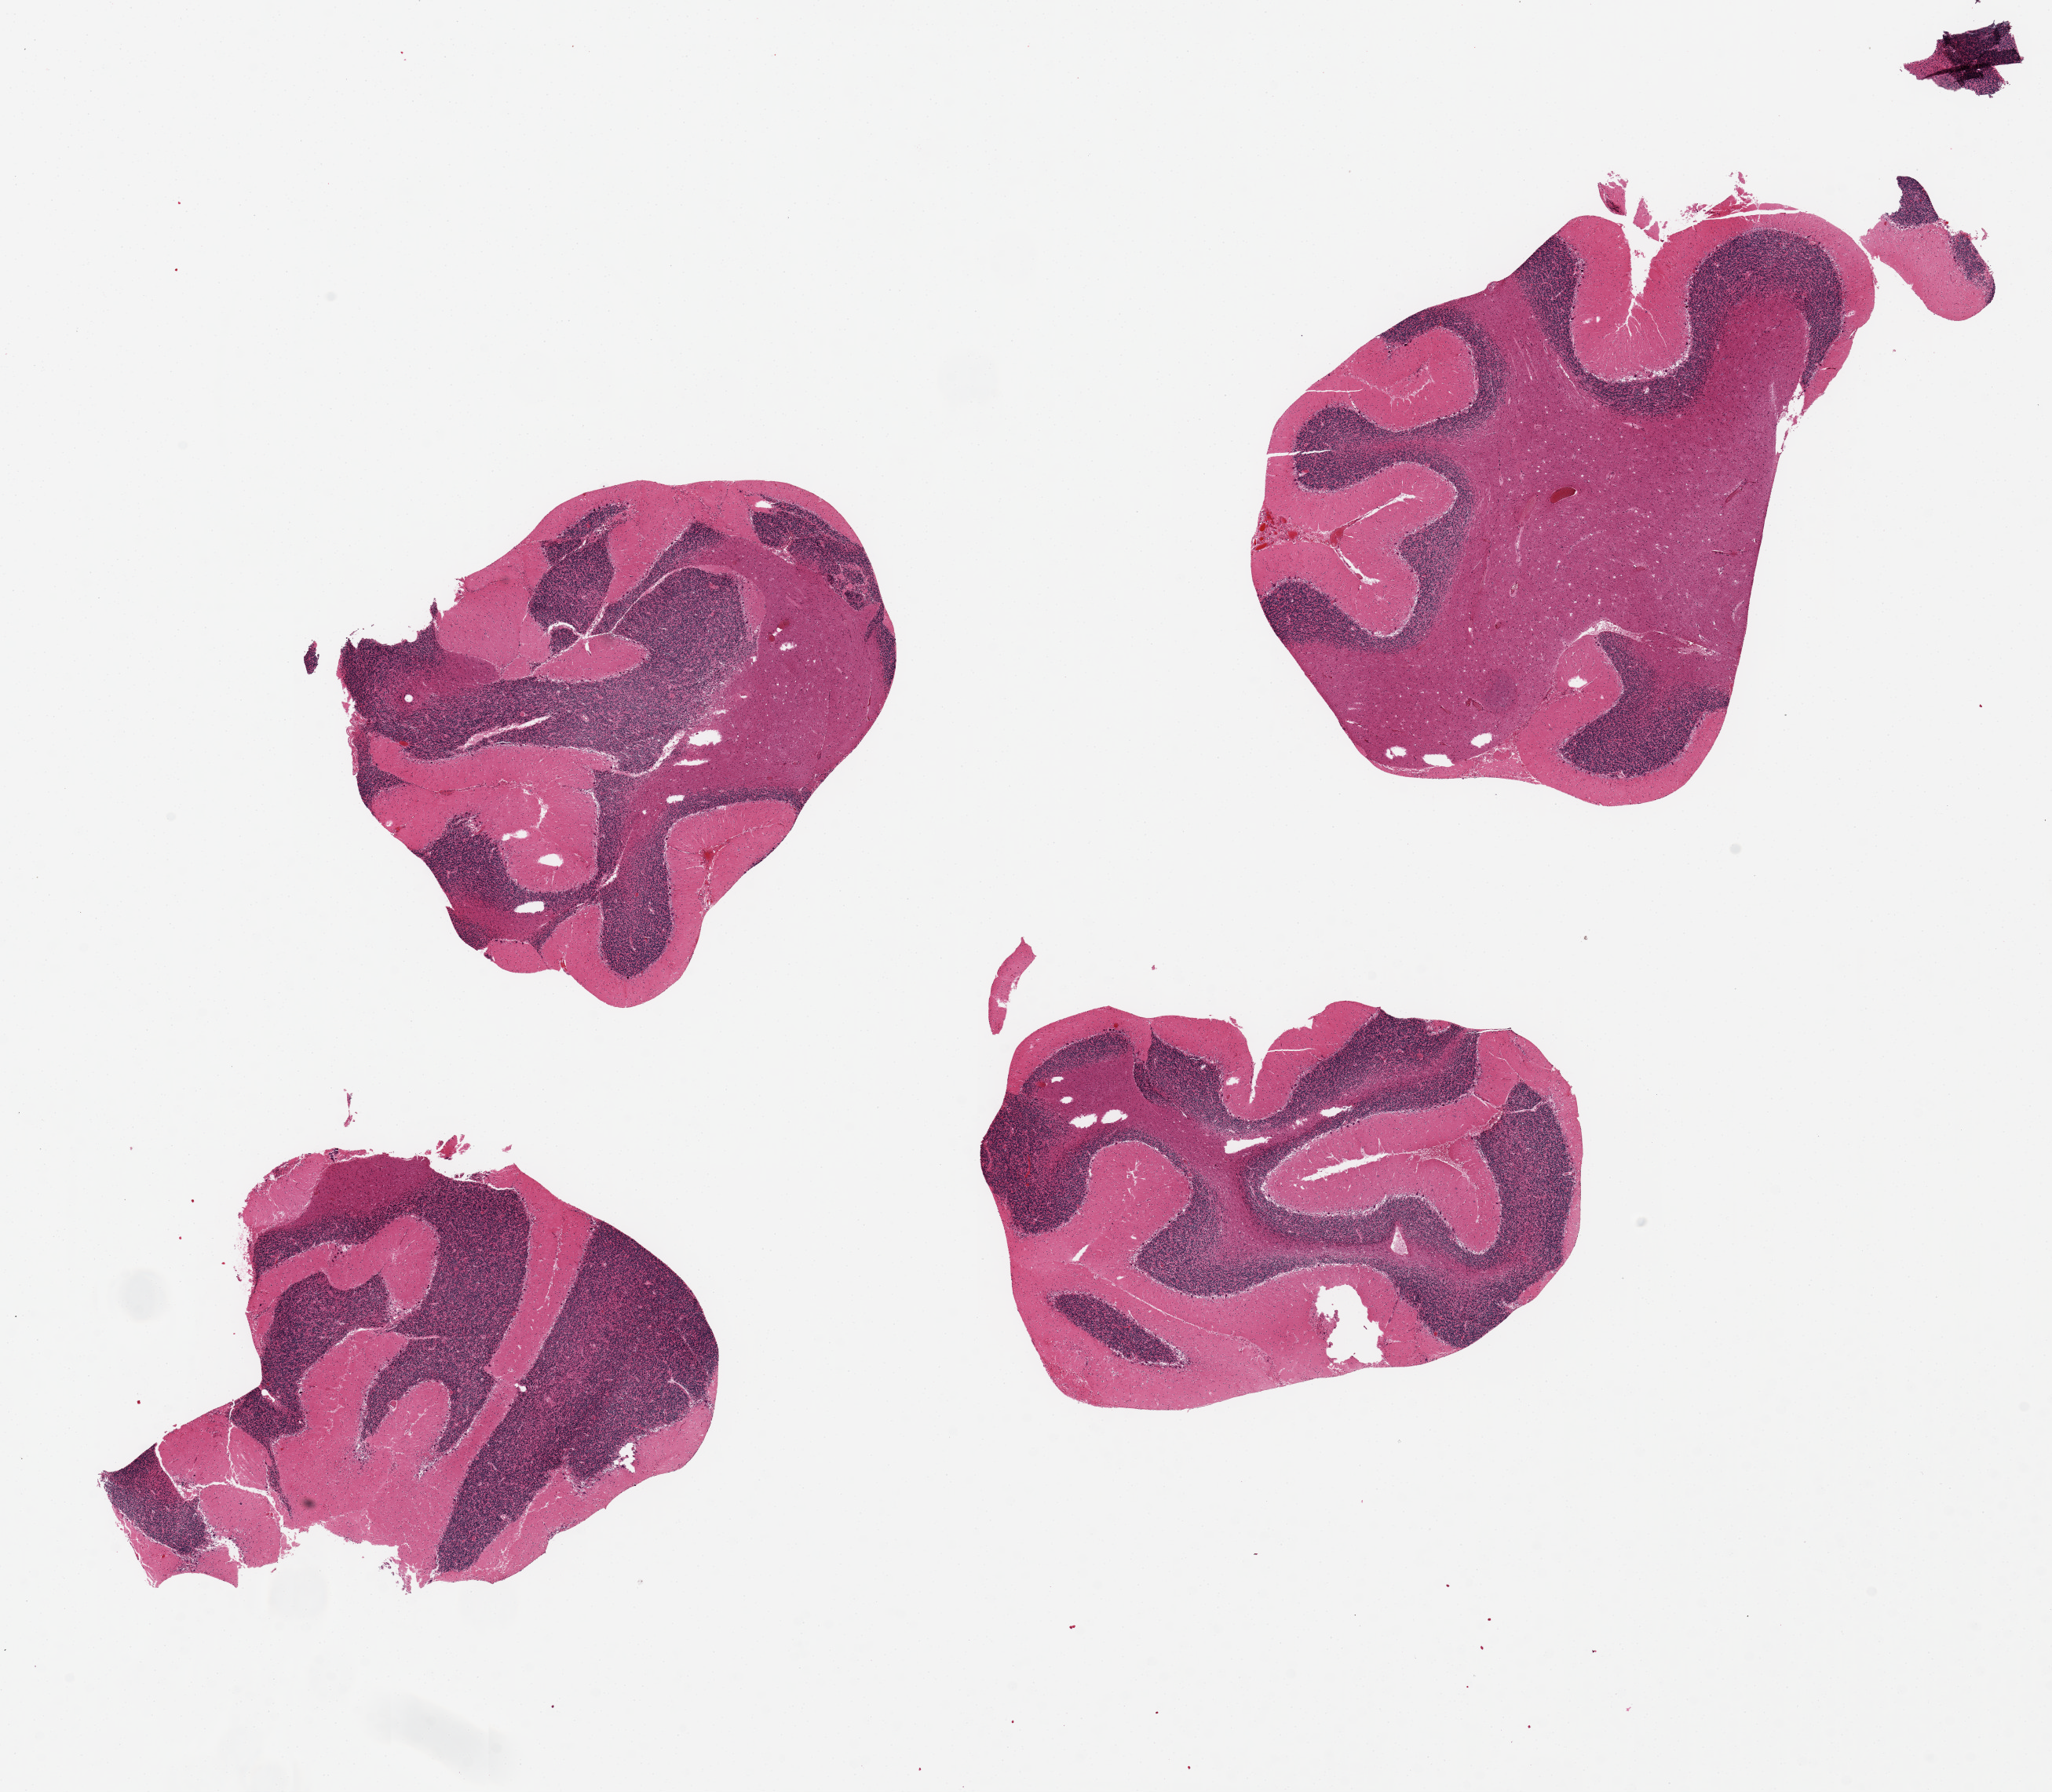
Digitized hematoxylin and eosin (H&E)-stained section — low-resolution overview of the scanned area, about 20.7 x 18.1 mm; PAXgene-fixed paraffin-embedded (PFPE) section; sampled site (target tissue): cerebellum; tissue donor sample. Donor sex: female.
- pathologist's review note for this sample: 4 ~6x5mm aliquots